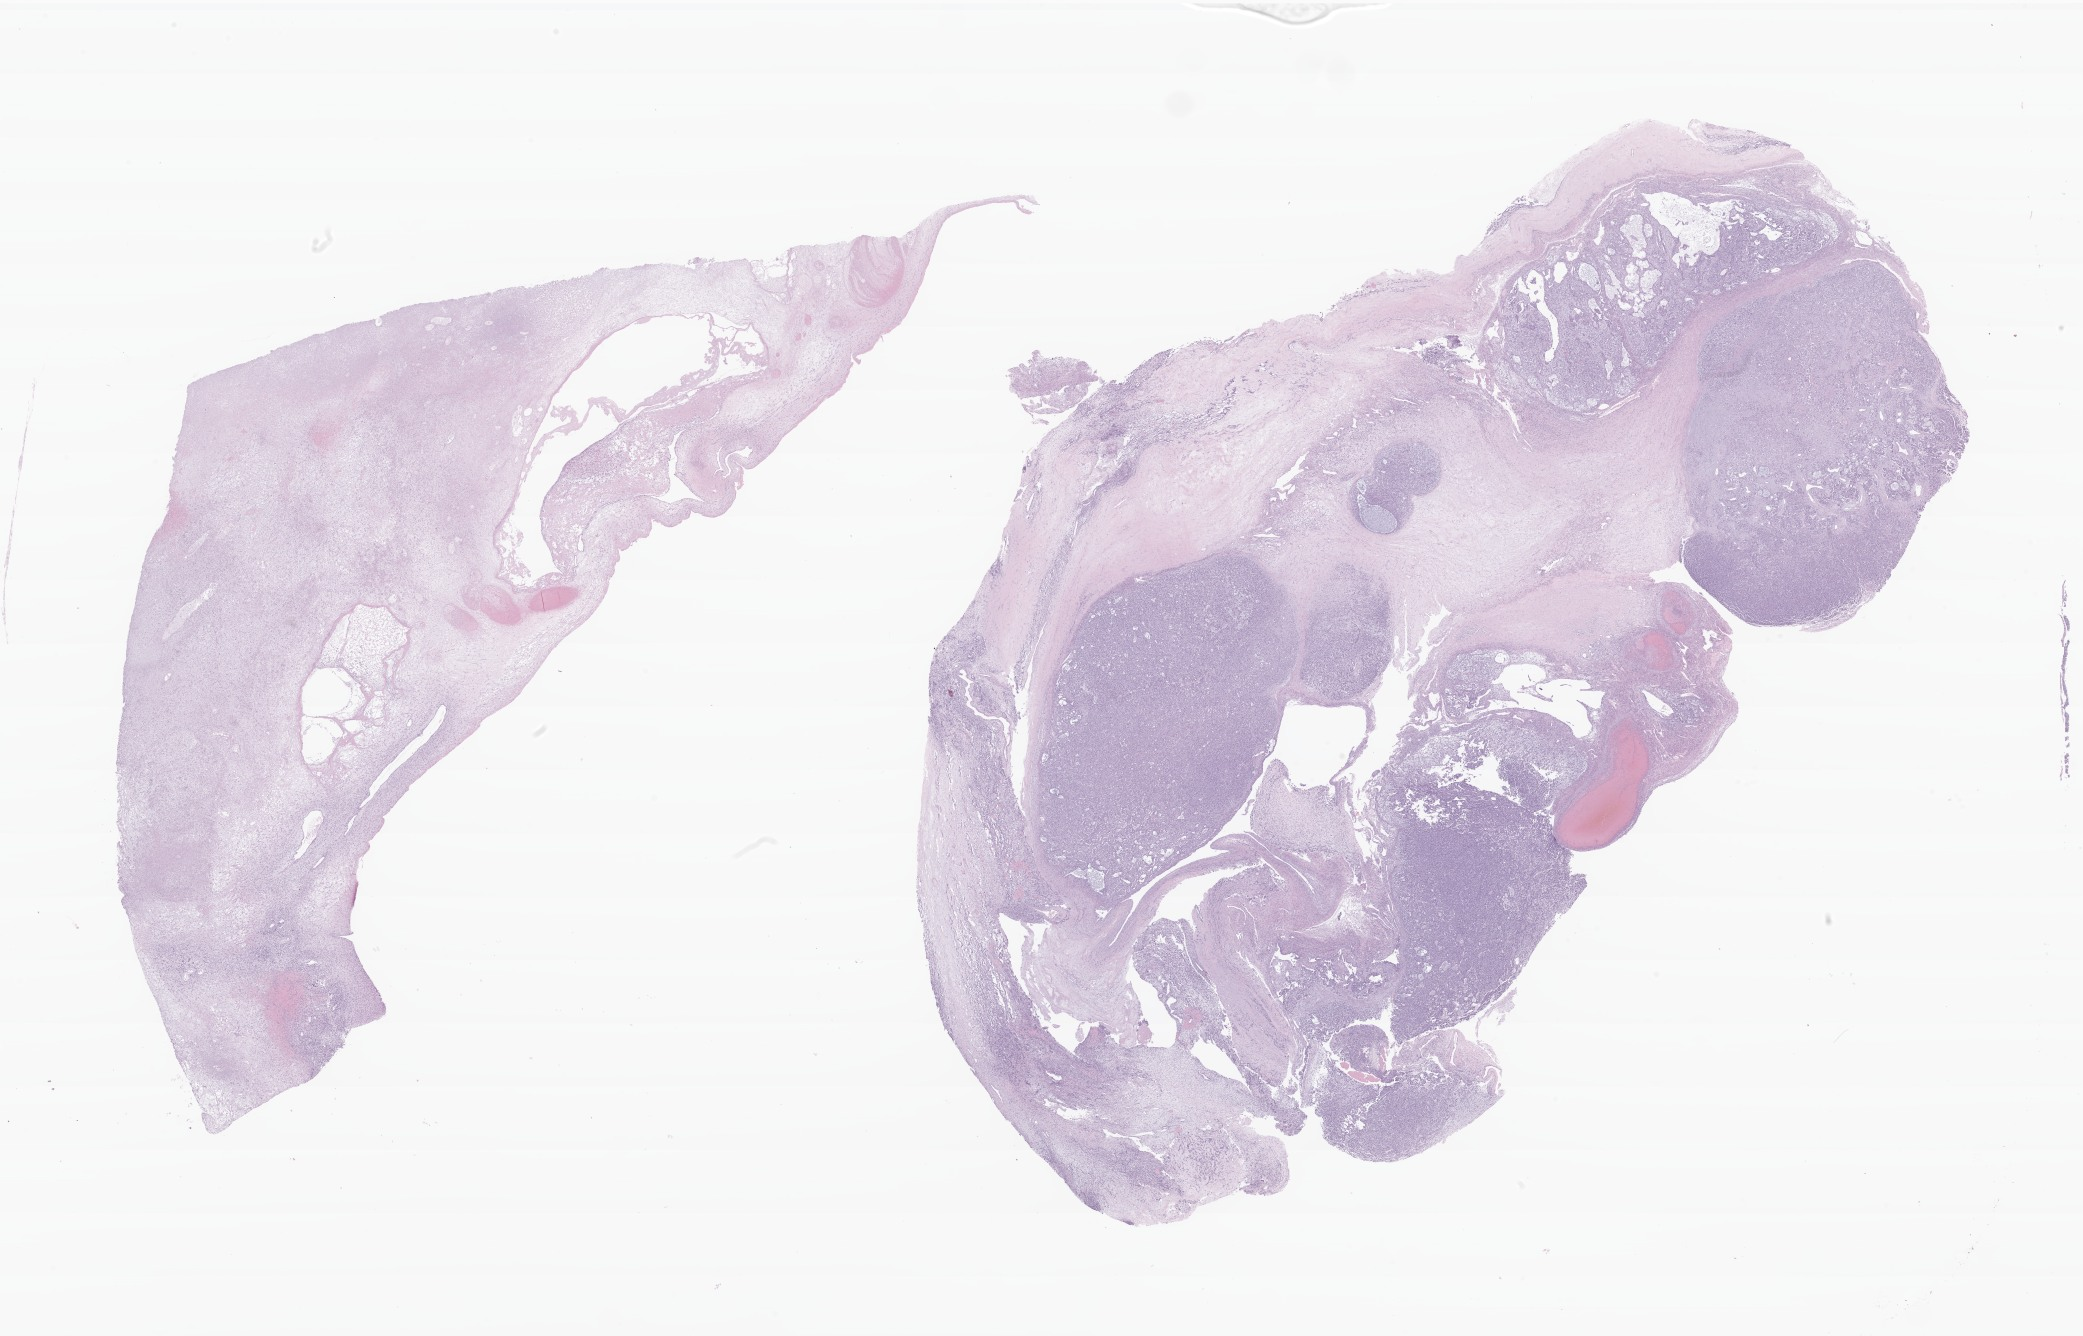
H&E whole-slide image of tumor tissue from the ovary, a low-resolution overview of the entire scanned area, about 35.0 x 22.5 mm, formalin-fixed, paraffin-embedded (FFPE) tissue. Female patient, age 212 months (17 years 8 months).
Diagnosis: Sex cord-gonadal stromal tumor, NOS.